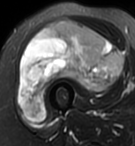
MRI of an extremity soft-tissue mass, one axial slice; T2-weighted fat-saturated; MR volume resampled by the dataset authors to the PET/CT grid (not the native acquisition matrix); 135 × 146 image matrix, field of view 132 × 143 mm. Female patient. From the clinical record (not read from this slice): histological type: pleiomorphic undifferentiated sarcoma; grade: high; site of the primary tumour: right quadricep.
Structures marked on this image (expert contour drawn on MRI and transferred to this co-registered scan by the dataset authors):
- gross tumour volume including surrounding oedema: bounding box (x1, y1, x2, y2) in pixels: (19, 20, 122, 122)
- gross tumour volume (mass): (19, 20, 122, 122)